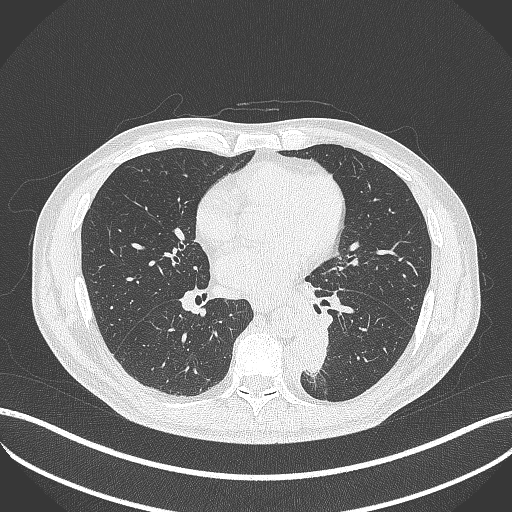
Chest CT, one axial slice. Position 191 of 451 along the scan axis. 120 kVp. Lung window (W 1500 / L -600 HU). 1 mm slice thickness. 512 × 512 image matrix. Male patient, age 72 years. From the clinical record (not read from this slice): clinical TNM (as recorded): T2b N0 M1.
Structures marked on this image (rectangle marked by the reading radiologist):
- lung tumour (recorded histology: adenocarcinoma): bounding box <301,329,330,385> (left, top, right, bottom; pixels)